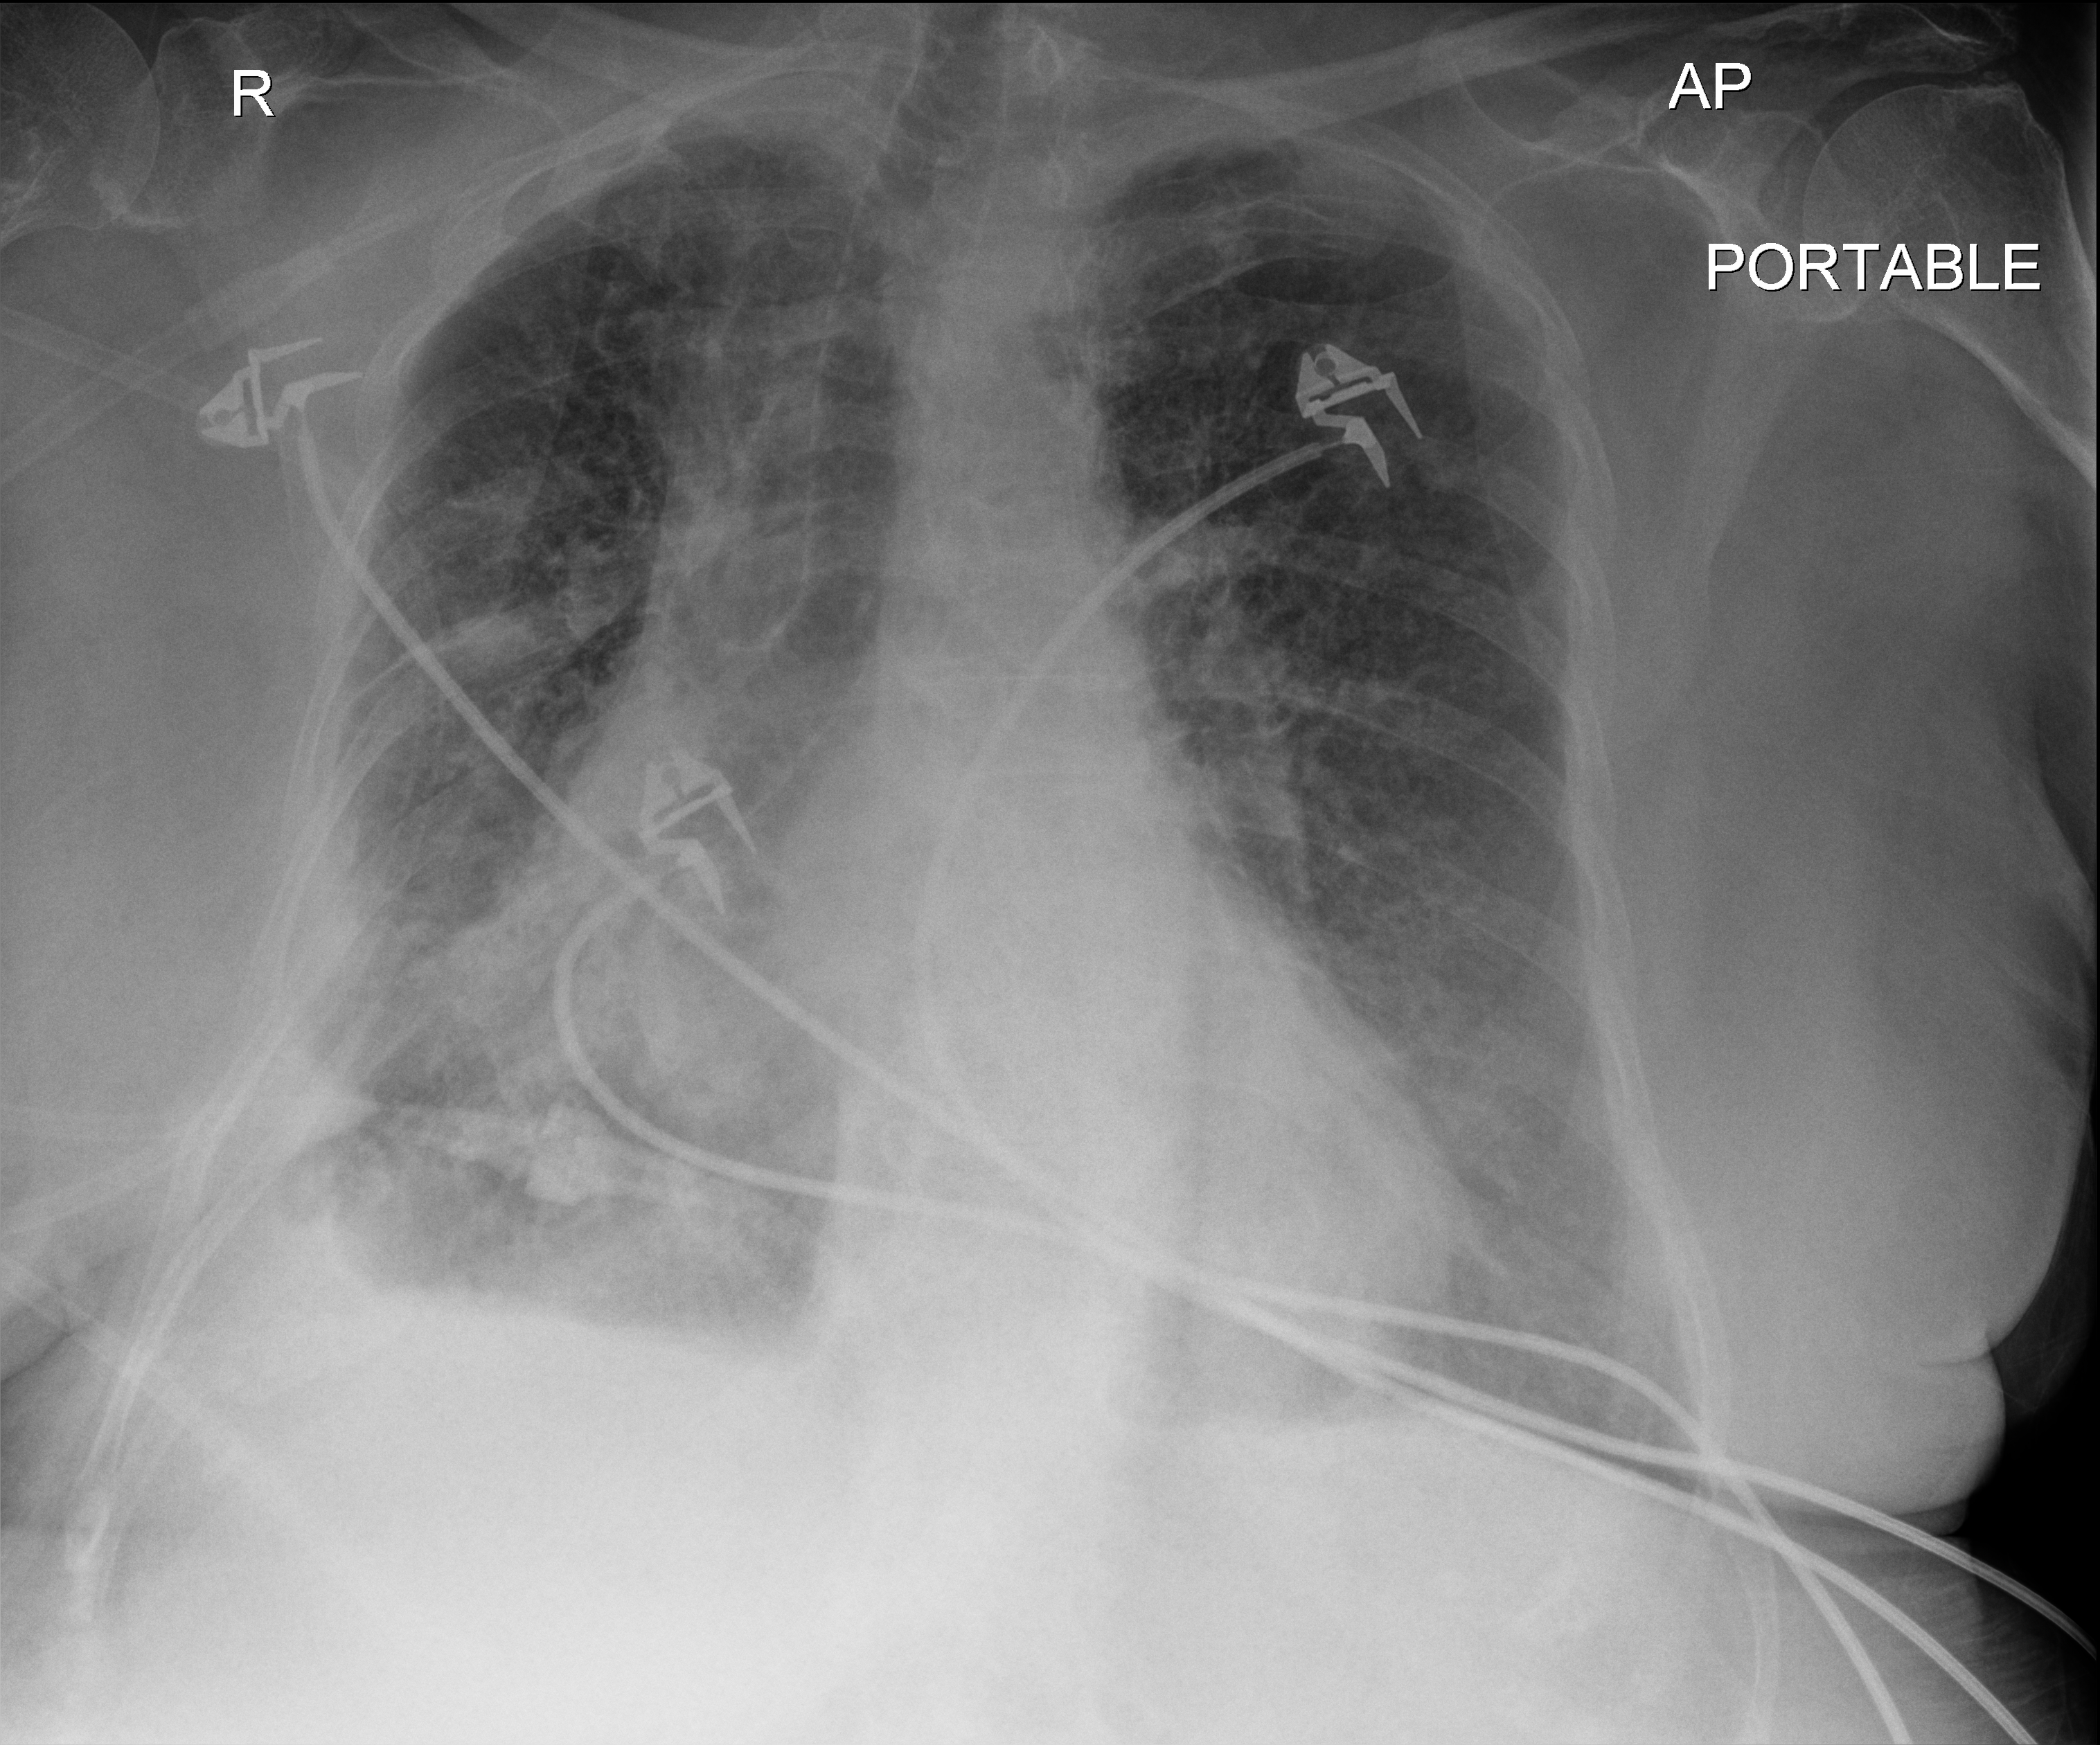
Chest radiograph. Female patient hospitalised with COVID-19, age 75–90 years.
Hospital-stay facts (about this admission, not read from this image; timing relative to this image not recorded): length of hospital stay: 9 days.